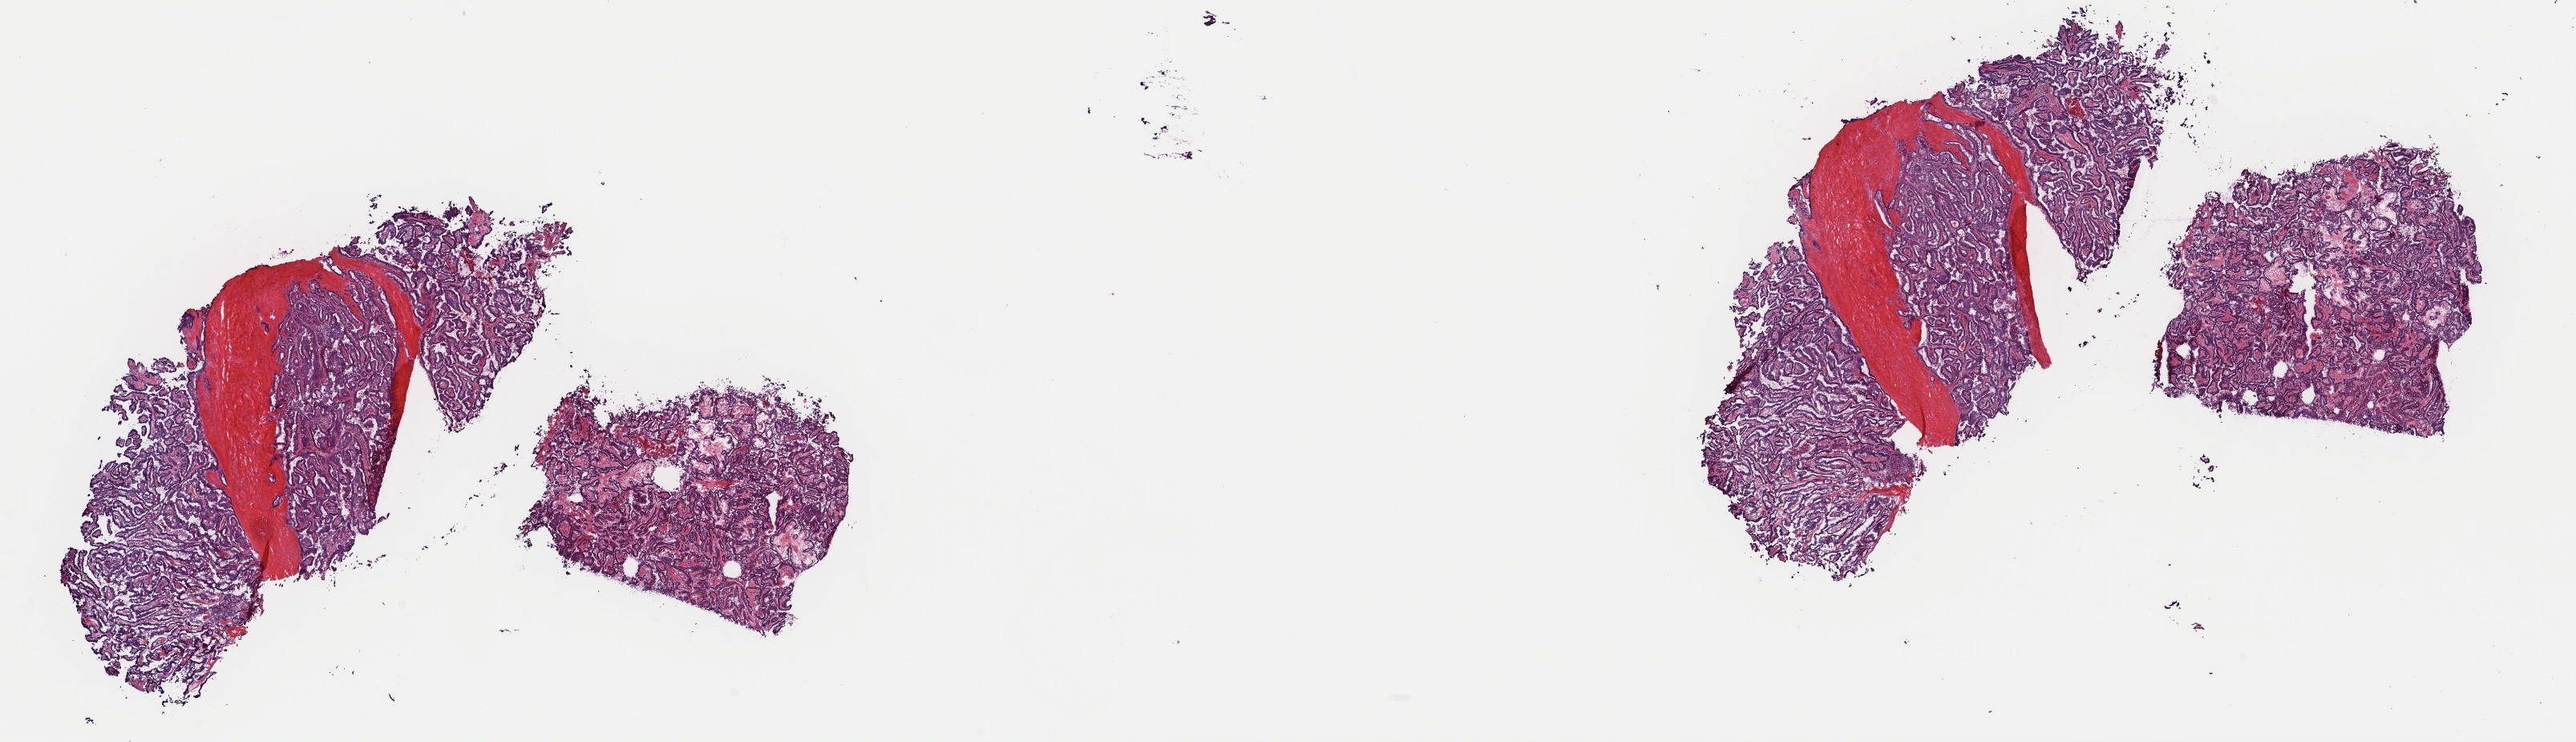
Digitized H&E tissue section (whole slide) — a low-resolution overview of the entire scanned area, about 25.4 x 7.3 mm, frozen section from the top of the tissue portion, primary tumour sample from the thyroid. Female, age 34 years at initial diagnosis. Slide review estimates, as recorded: tumour cells 85%, tumour nuclei 70%, normal cells 0%, stromal cells 15%, necrosis 0%. Infiltration values recorded for this section: lymphocyte infiltration 0%, monocyte infiltration 0%, neutrophil infiltration 0%.
Laterality: right. AJCC pathologic stage: I (7th edition). Pathologic diagnosis: Papillary adenocarcinoma, NOS (thyroid gland).